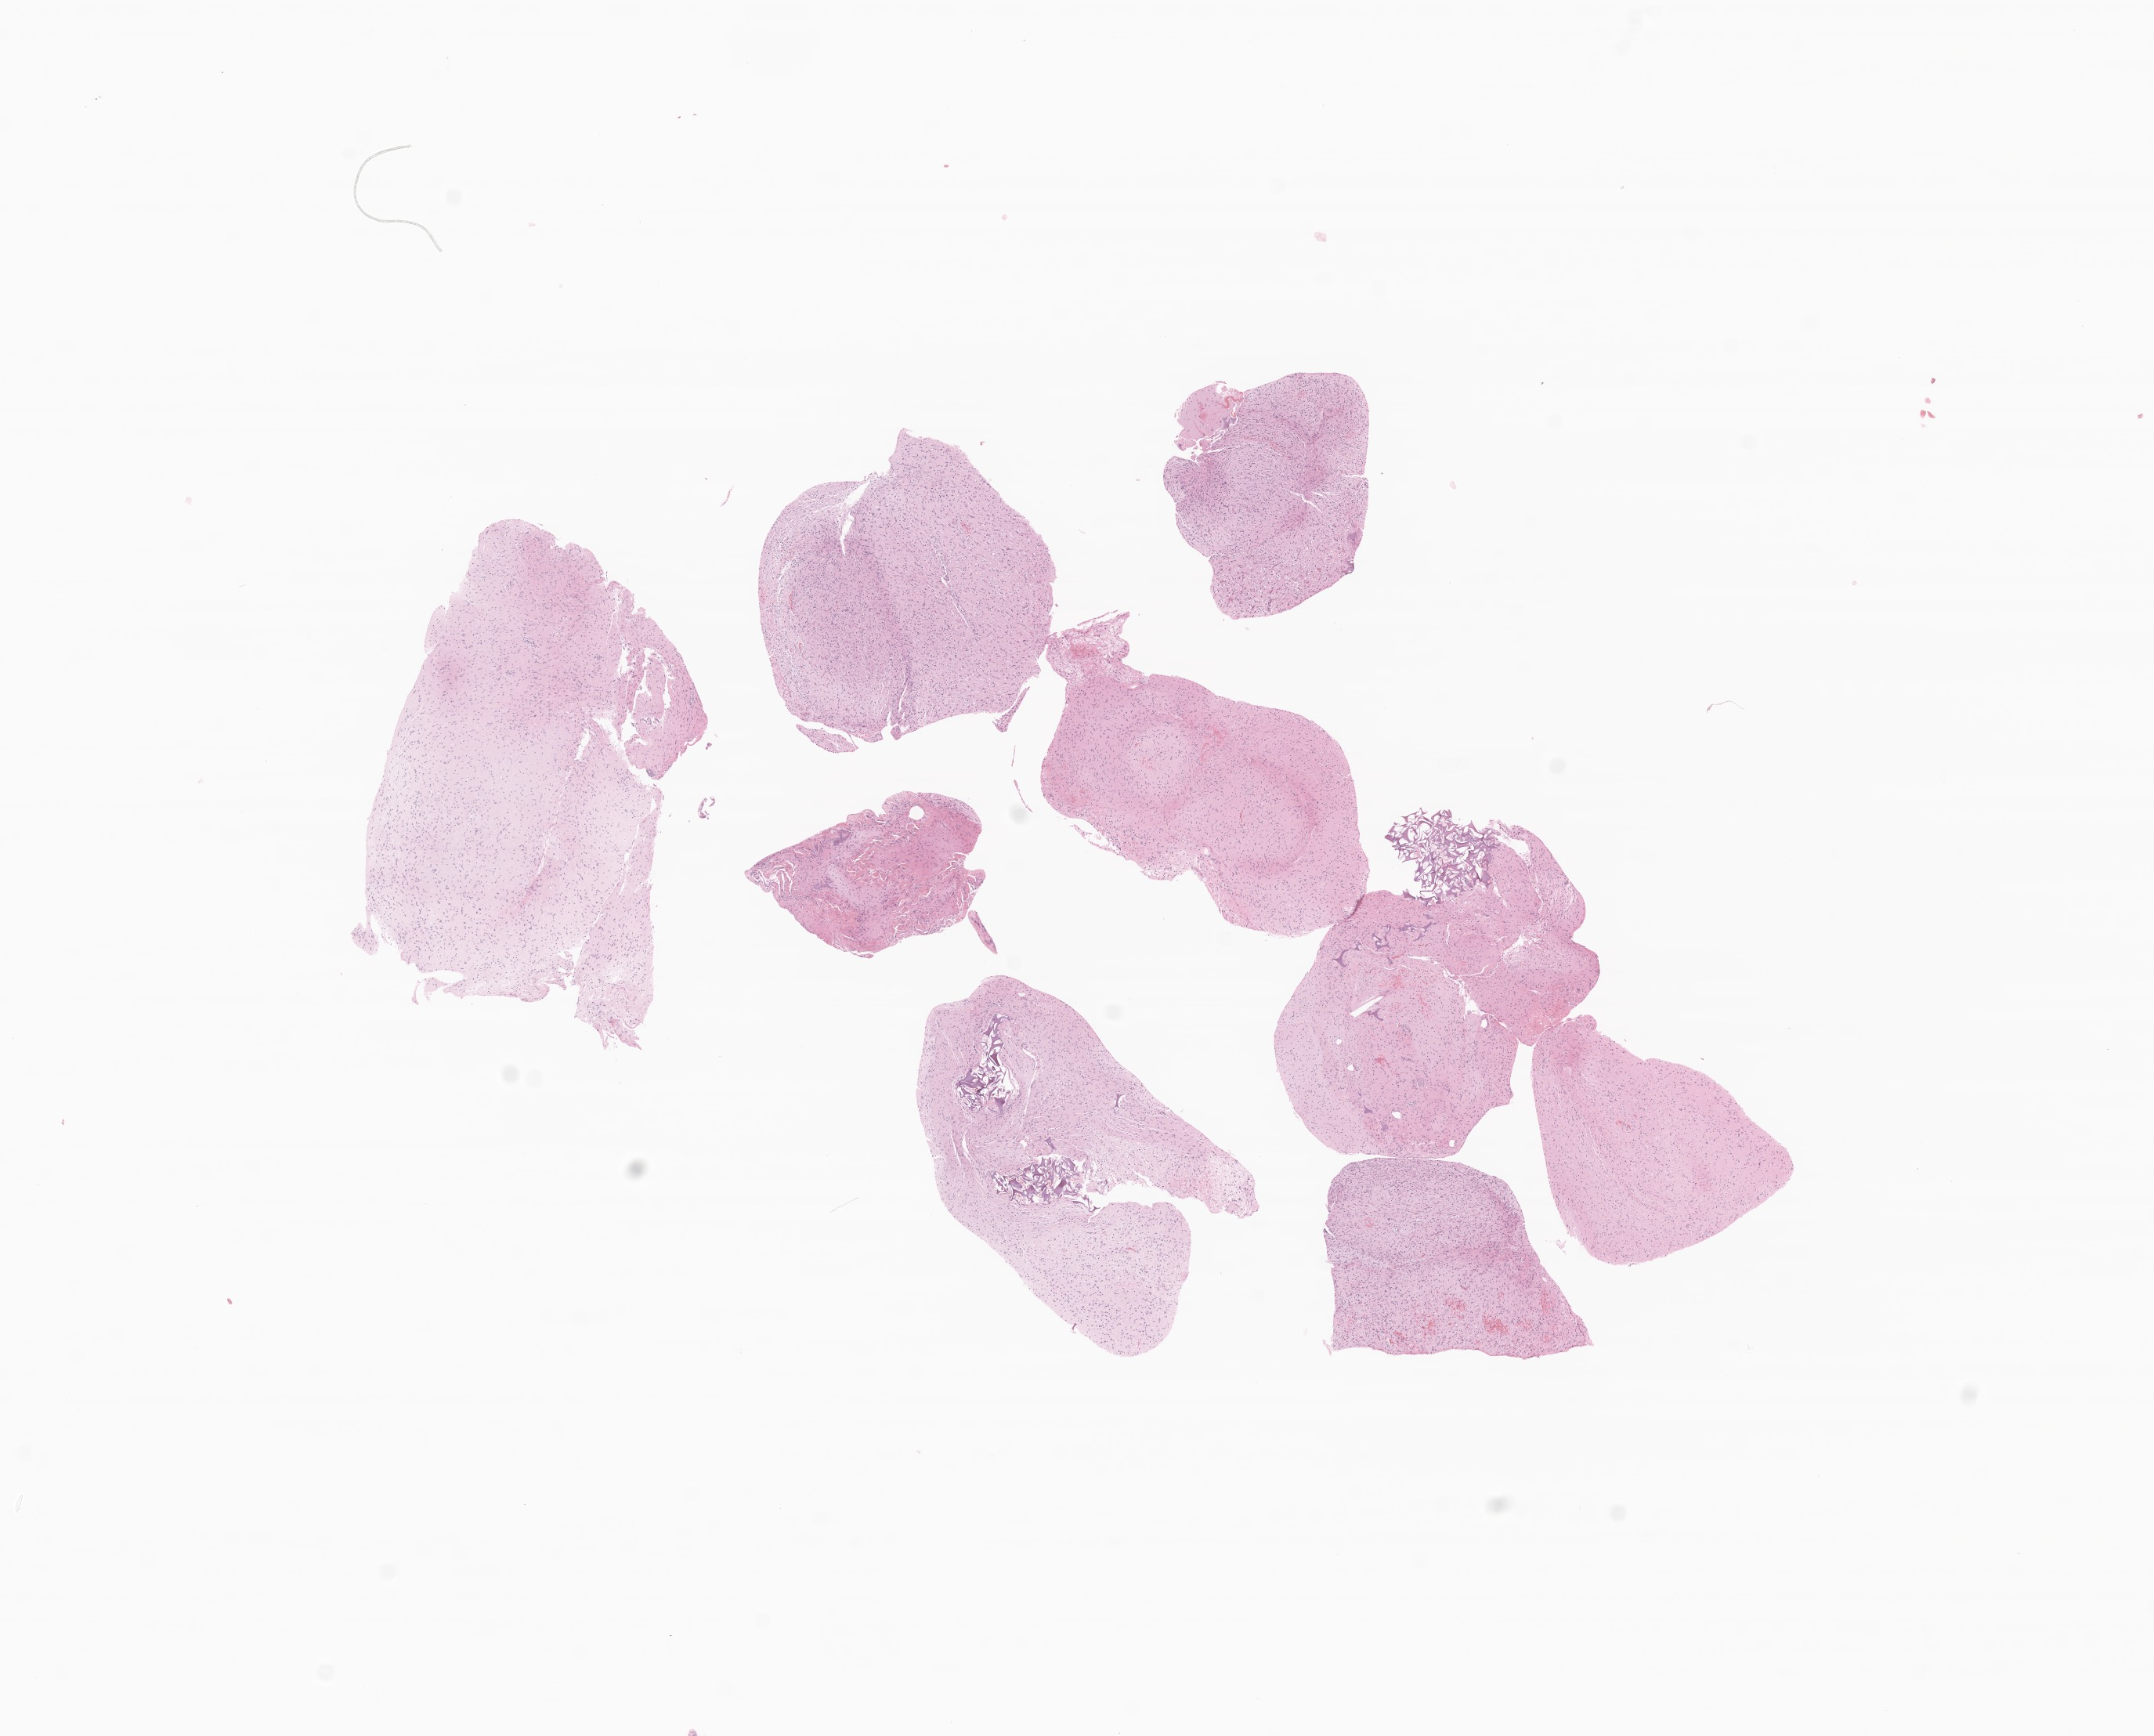
H&E whole-slide image of tumor tissue from the brain — shown as a low-resolution overview of the whole scanned area (about 11.6 x 9.3 mm), FFPE section. Patient male; age 71 months (5 years 11 months).
Recorded diagnosis: Glioma, malignant.